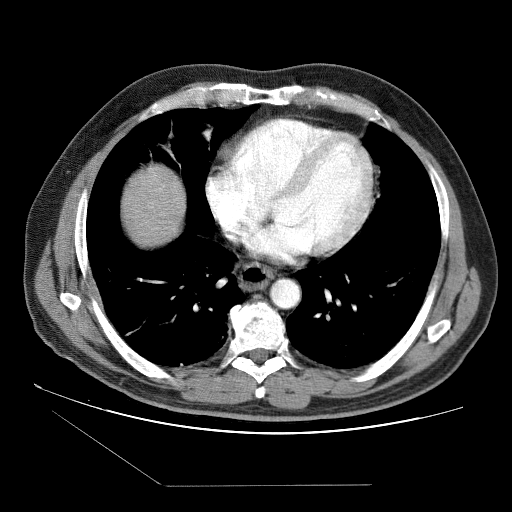
Contrast-enhanced abdominal CT (liver protocol), one axial slice. Slice 83 of 87 in the series (ordered by position). Reconstruction kernel STANDARD. 120 kVp. Soft-tissue window (W 400 / L 40 HU). 2.5 mm slice thickness. 512 × 512 image matrix, field of view 400 × 400 mm. From the clinical record (not read from this slice): diagnosis: hepatocellular carcinoma (patient treated with transarterial chemoembolisation; whether this scan precedes or follows treatment is not stated here); TNM stage (as recorded): Stage-II; Child-Pugh class: B; tumour differentiation: no biopsy; tumour size: 2.6 cm.
Outlined on this slice (semi-automatic segmentation, software-assisted and operator-edited):
- liver parenchyma outside the tumour (the mass and vessels are separate outlines, so this box may not span the whole liver): bounding box [x1, y1, x2, y2] px = [122, 164, 184, 244]